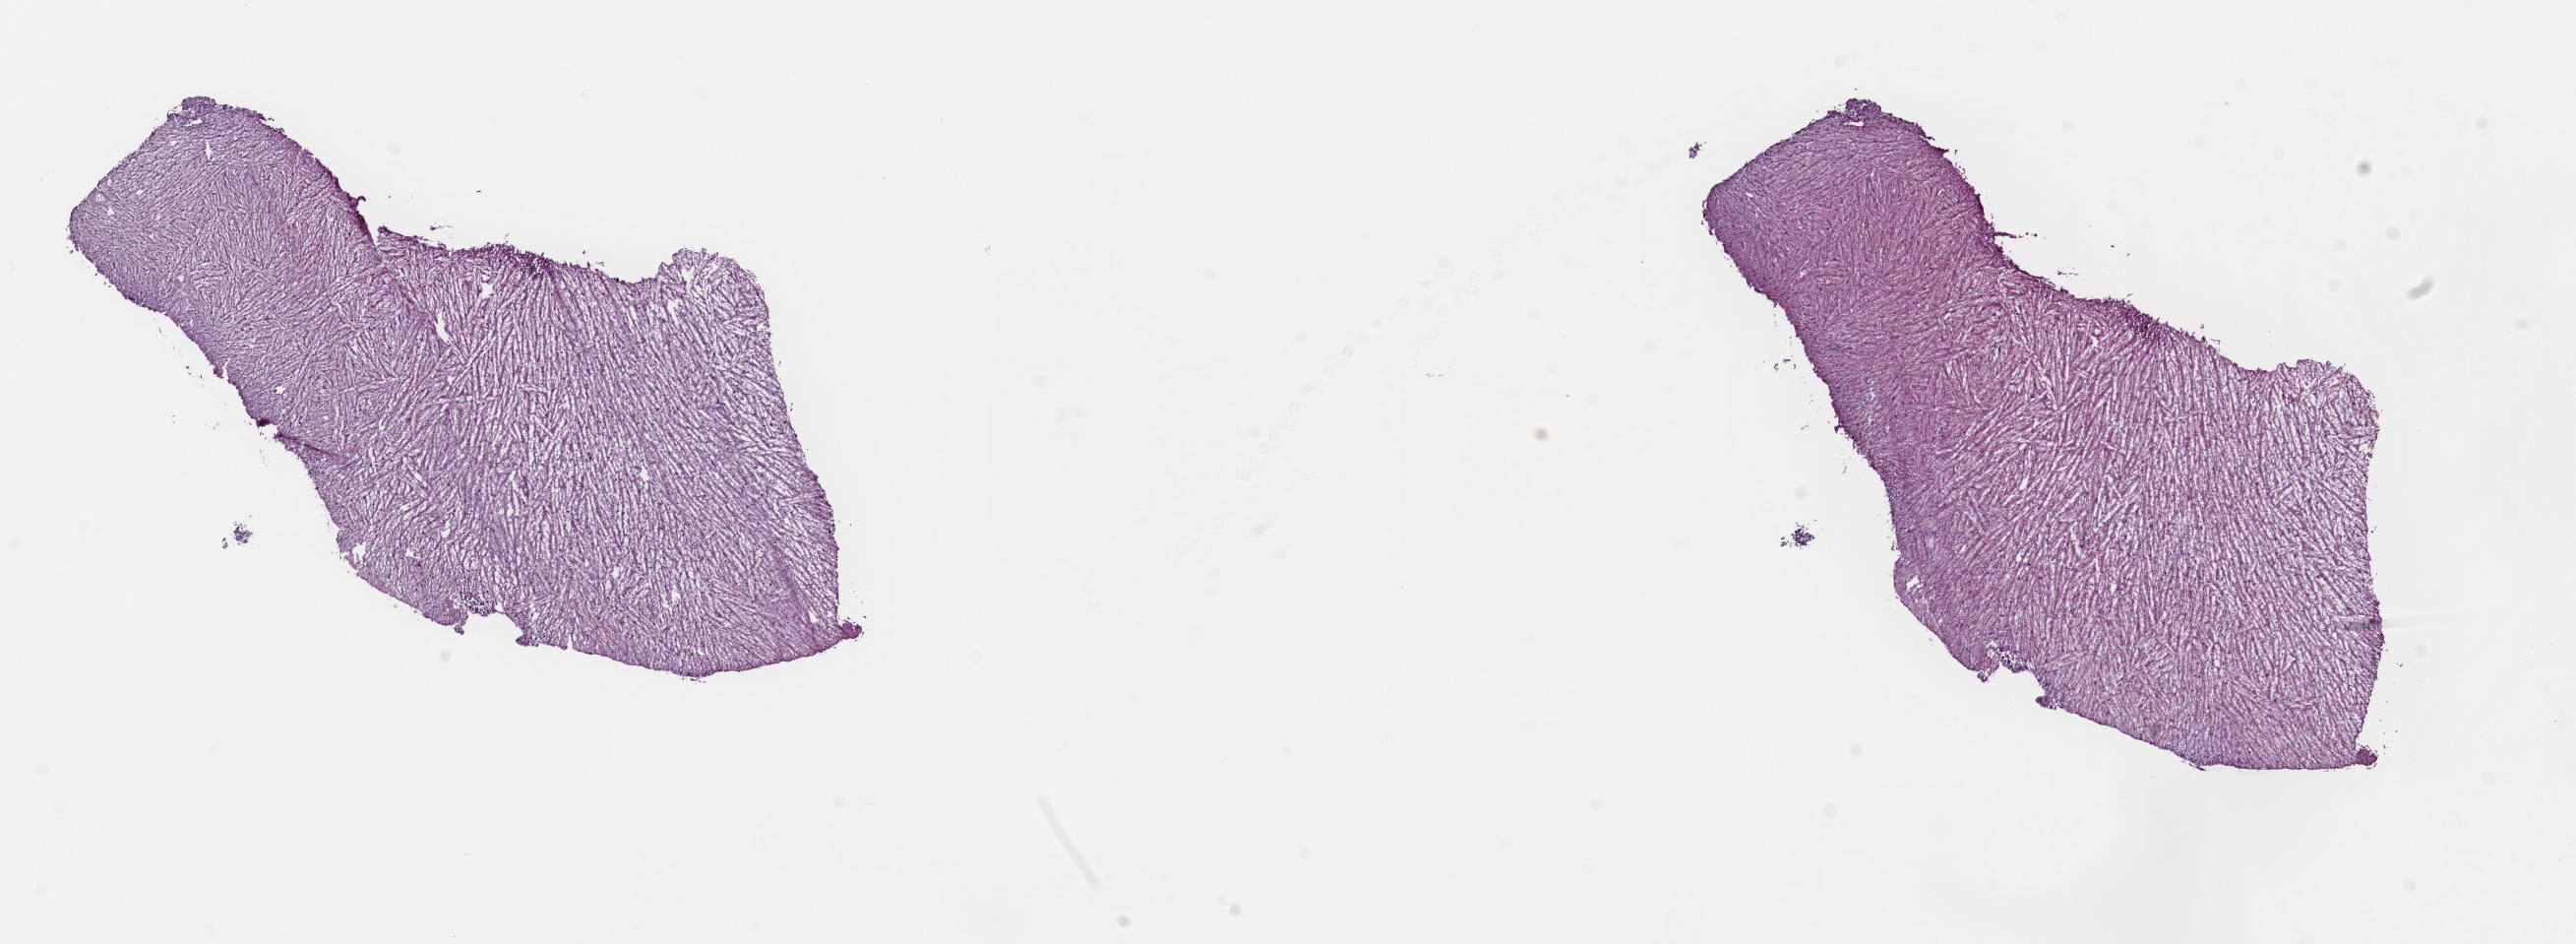
Whole-slide histology image, Hematoxylin and eosin (H&E) stained, whole scanned area (about 20.7 x 7.6 mm, from a 40x scan) shown as a low-resolution overview; frozen section from the top of the tissue portion; sample: primary tumour, brain. Male patient; age at initial diagnosis 66 years. Histologic grade: G2 (moderately differentiated). Composition of this section per pathologist review: tumour cells 40%, tumour nuclei 80%, normal cells 10%, stromal cells 50%, necrosis 0%. Inflammatory infiltration, as recorded: lymphocyte infiltration 0%, monocyte infiltration 0%, neutrophil infiltration 0%.
Histologic diagnosis: Astrocytoma, NOS (cerebrum).